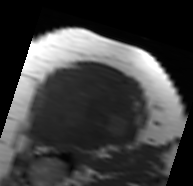
MRI of an extremity soft-tissue mass, one axial slice; slice 54 of 91 in the series (ordered by position); MR volume resampled by the dataset authors to the PET/CT grid (not the native acquisition matrix); 3.27 mm slice thickness; 193 × 186 image matrix, field of view 188 × 182 mm. Female patient. From the clinical record (not read from this slice): histological type: malignant solitary fibrous tumor; grade: intermediate; site of the primary tumour: right thigh.
Annotated regions visible in this slice (expert contour drawn on MRI and transferred to this co-registered scan by the dataset authors):
- gross tumour volume including surrounding oedema: bounding box <24,67,141,150> (left, top, right, bottom; pixels)
- gross tumour volume (mass): <24,69,137,148>